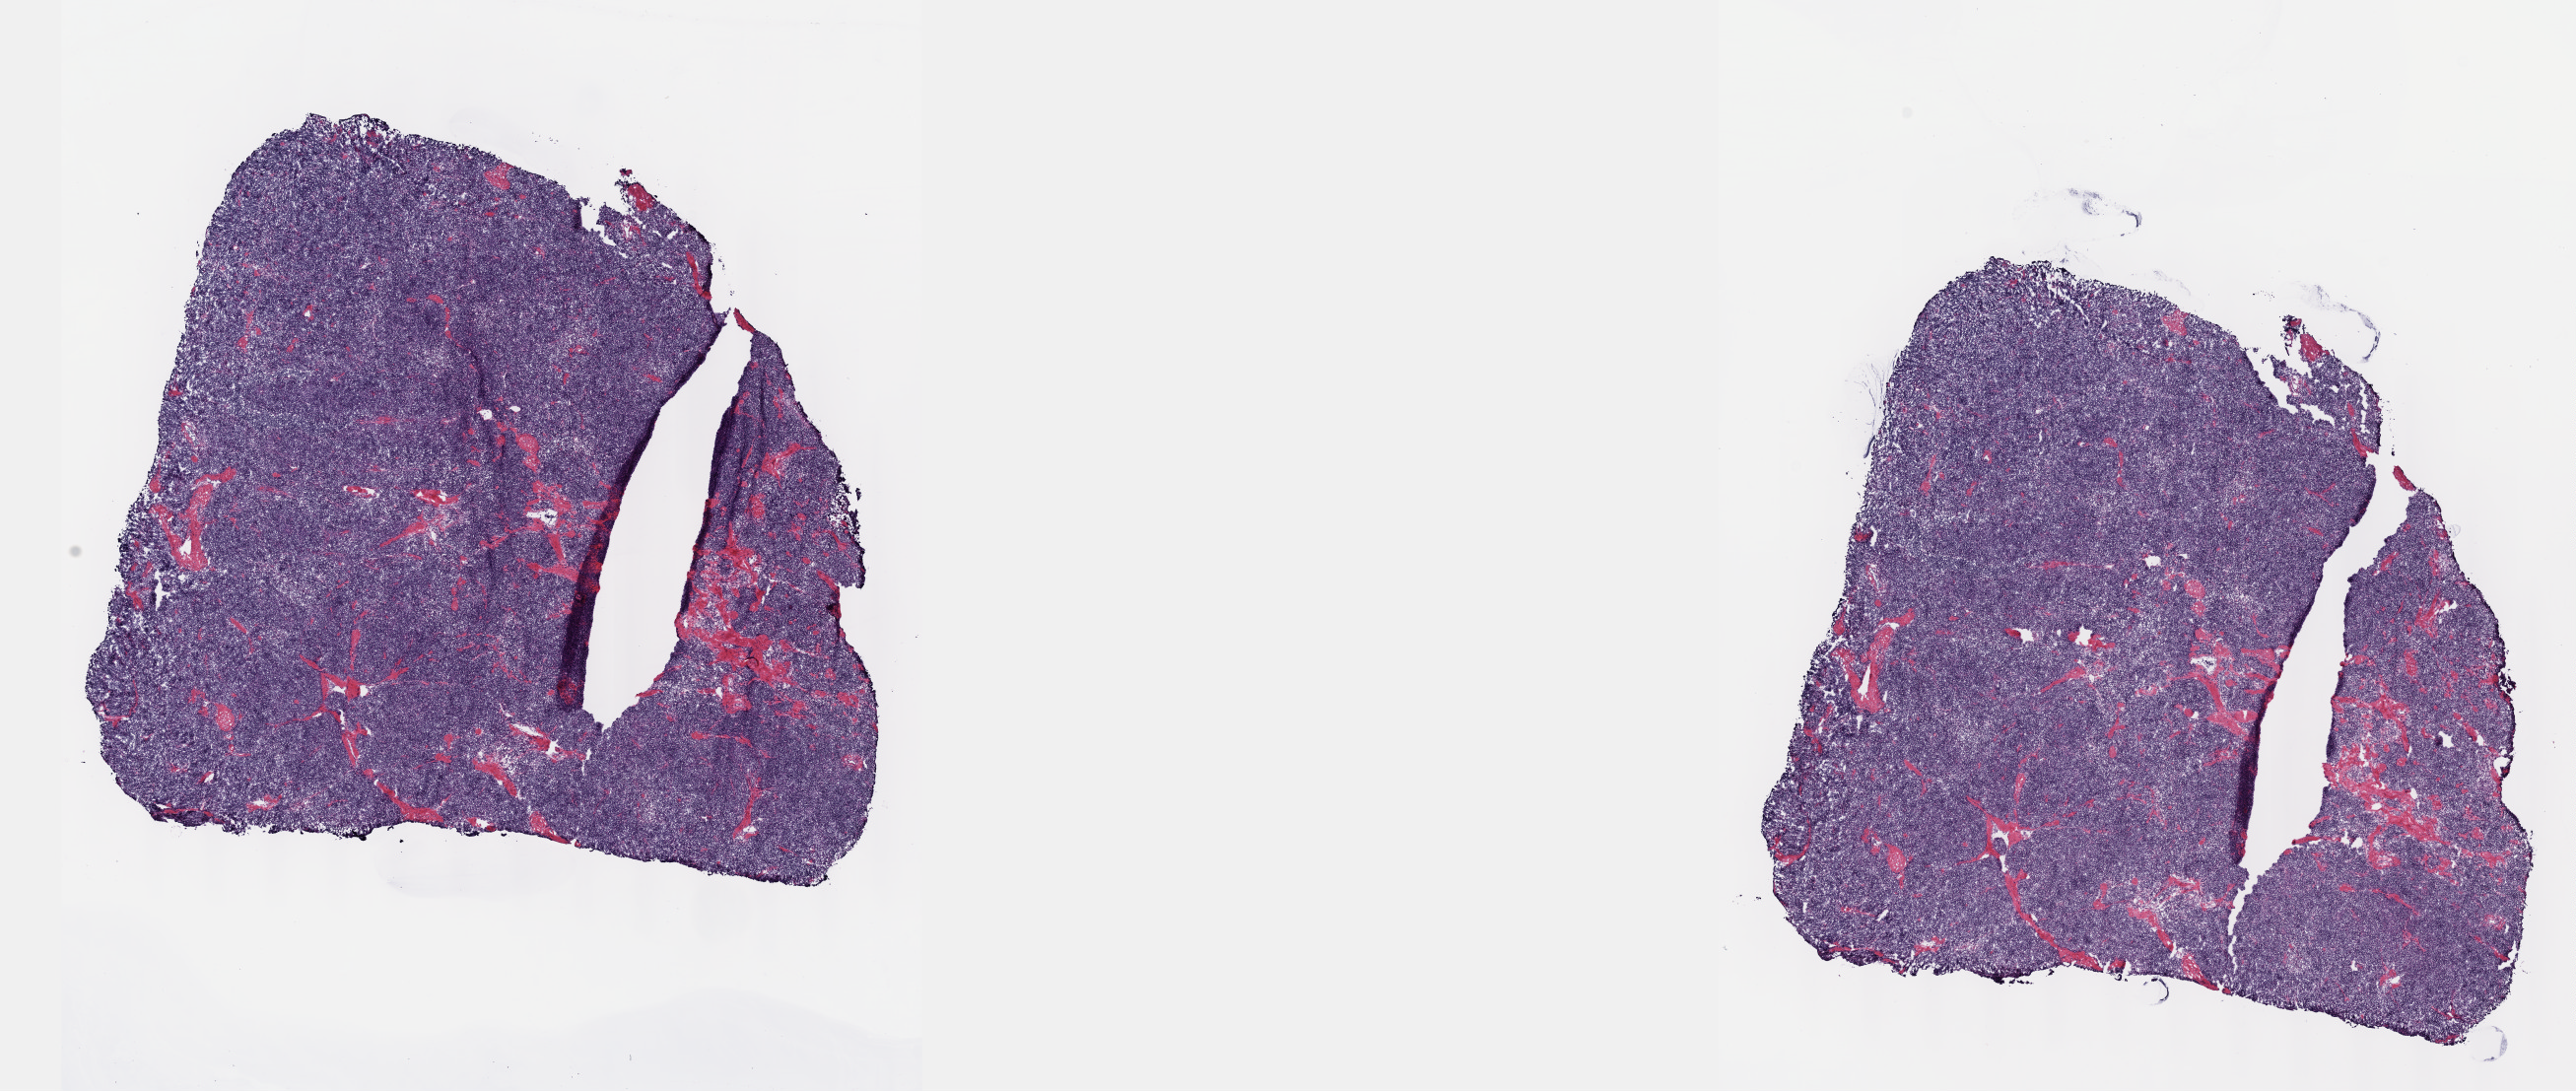
Digitized H&E-stained tissue section (whole slide) — shown as a low-resolution overview of the whole scanned area (about 21.1 x 8.9 mm, slide scanned at 40x), frozen section, thymus, primary tumour sample. Patient: male, age at initial diagnosis 45 years. Composition of this section per pathologist review: tumour cells 100%, tumour nuclei 80%, normal cells 0%, stromal cells 0%, necrosis 0%. Inflammatory infiltration, as recorded: lymphocyte infiltration 2%, monocyte infiltration 0%, neutrophil infiltration 0%.
• histologic diagnosis: Thymoma, type B2, NOS